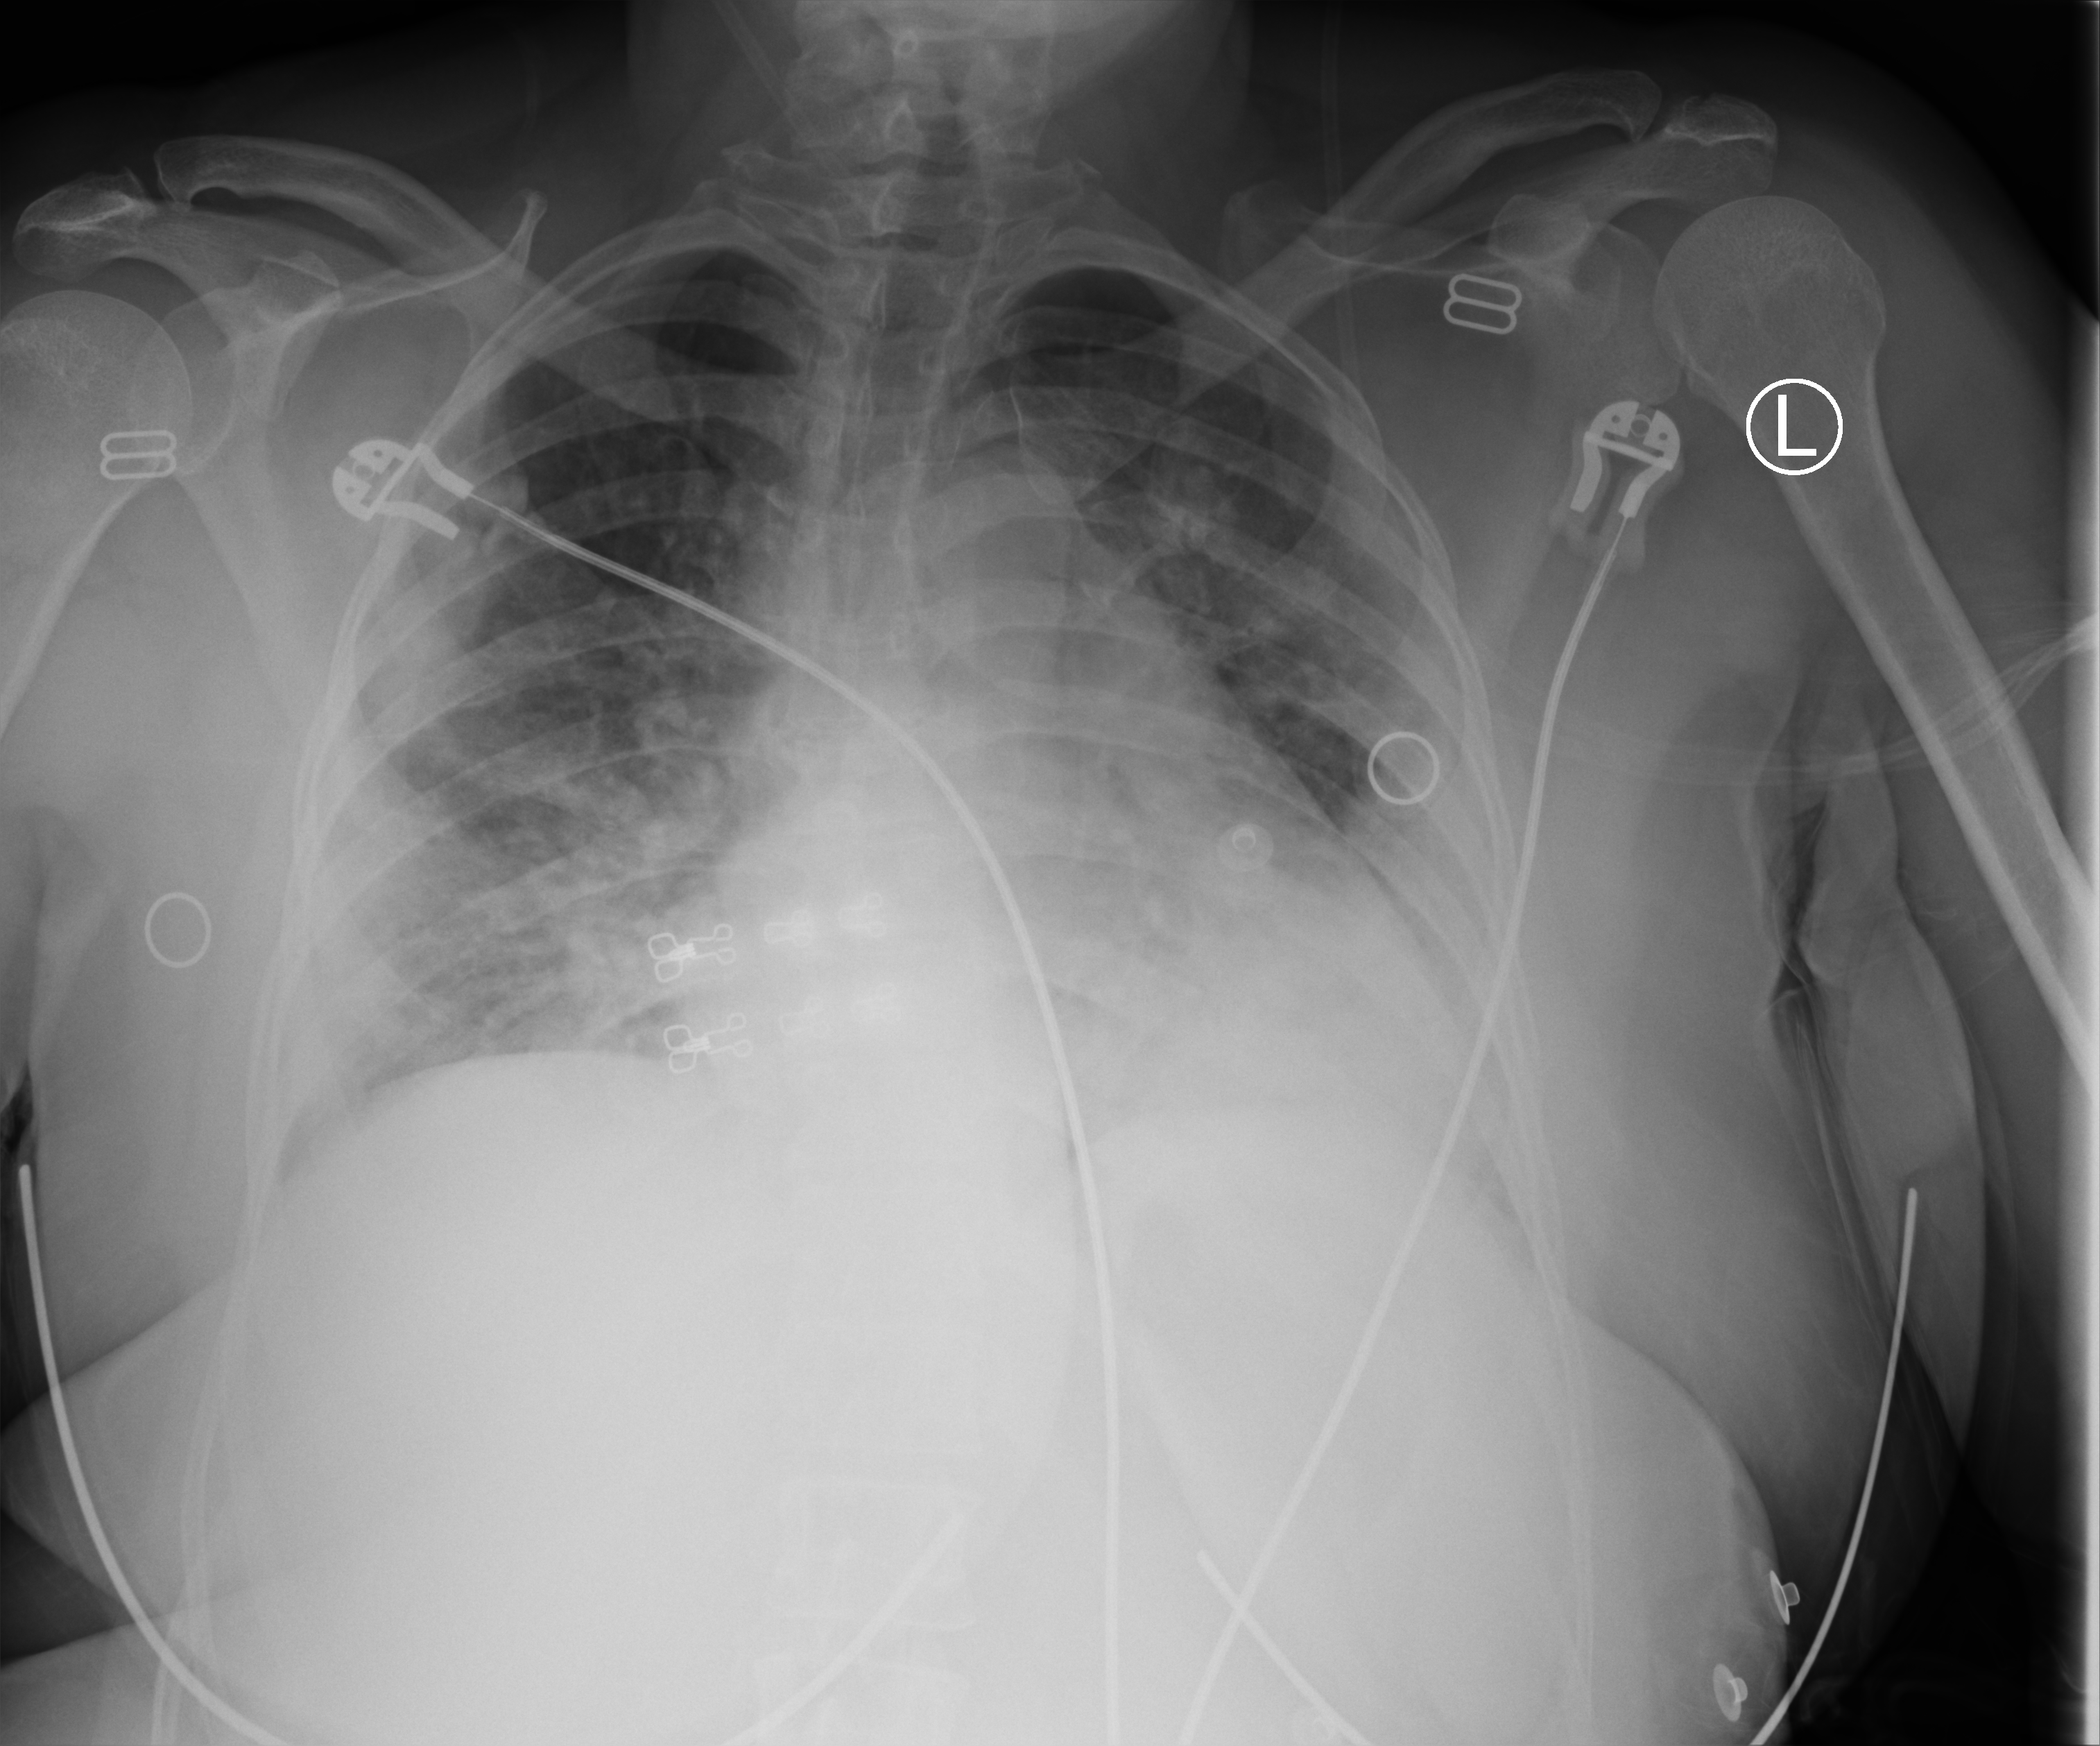
Portable chest radiograph; anteroposterior (AP) projection. Female patient hospitalised with COVID-19, age 18–59 years.
From the hospital-stay record, not from the radiograph (when in the stay this image was taken is not recorded): mechanically ventilated during this hospital stay: no.